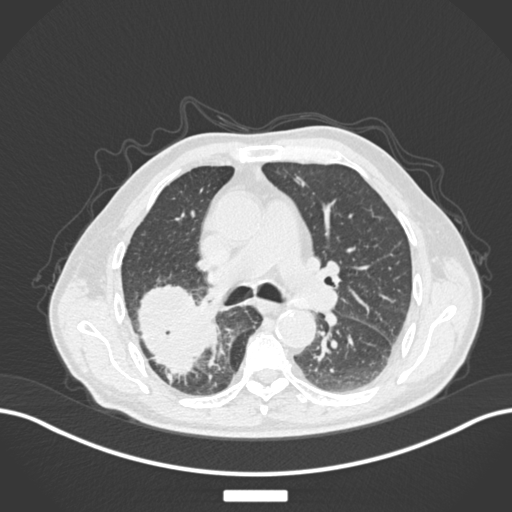
Chest CT, one axial slice. Position 105 of 201 along the scan axis. Reconstruction kernel B30f. 120 kVp. Lung window (W 1500 / L -600 HU). 1 mm slice thickness. 512 × 512 image matrix, field of view 400 × 400 mm. Male patient, age 72 years. From the clinical record (not read from this slice): clinical TNM (as recorded): T3 N2 M0.
Structures marked on this image (rectangle marked by the reading radiologist):
- lung tumour (recorded histology: adenocarcinoma): bounding box (x1, y1, x2, y2) in pixels: (130, 284, 217, 380)